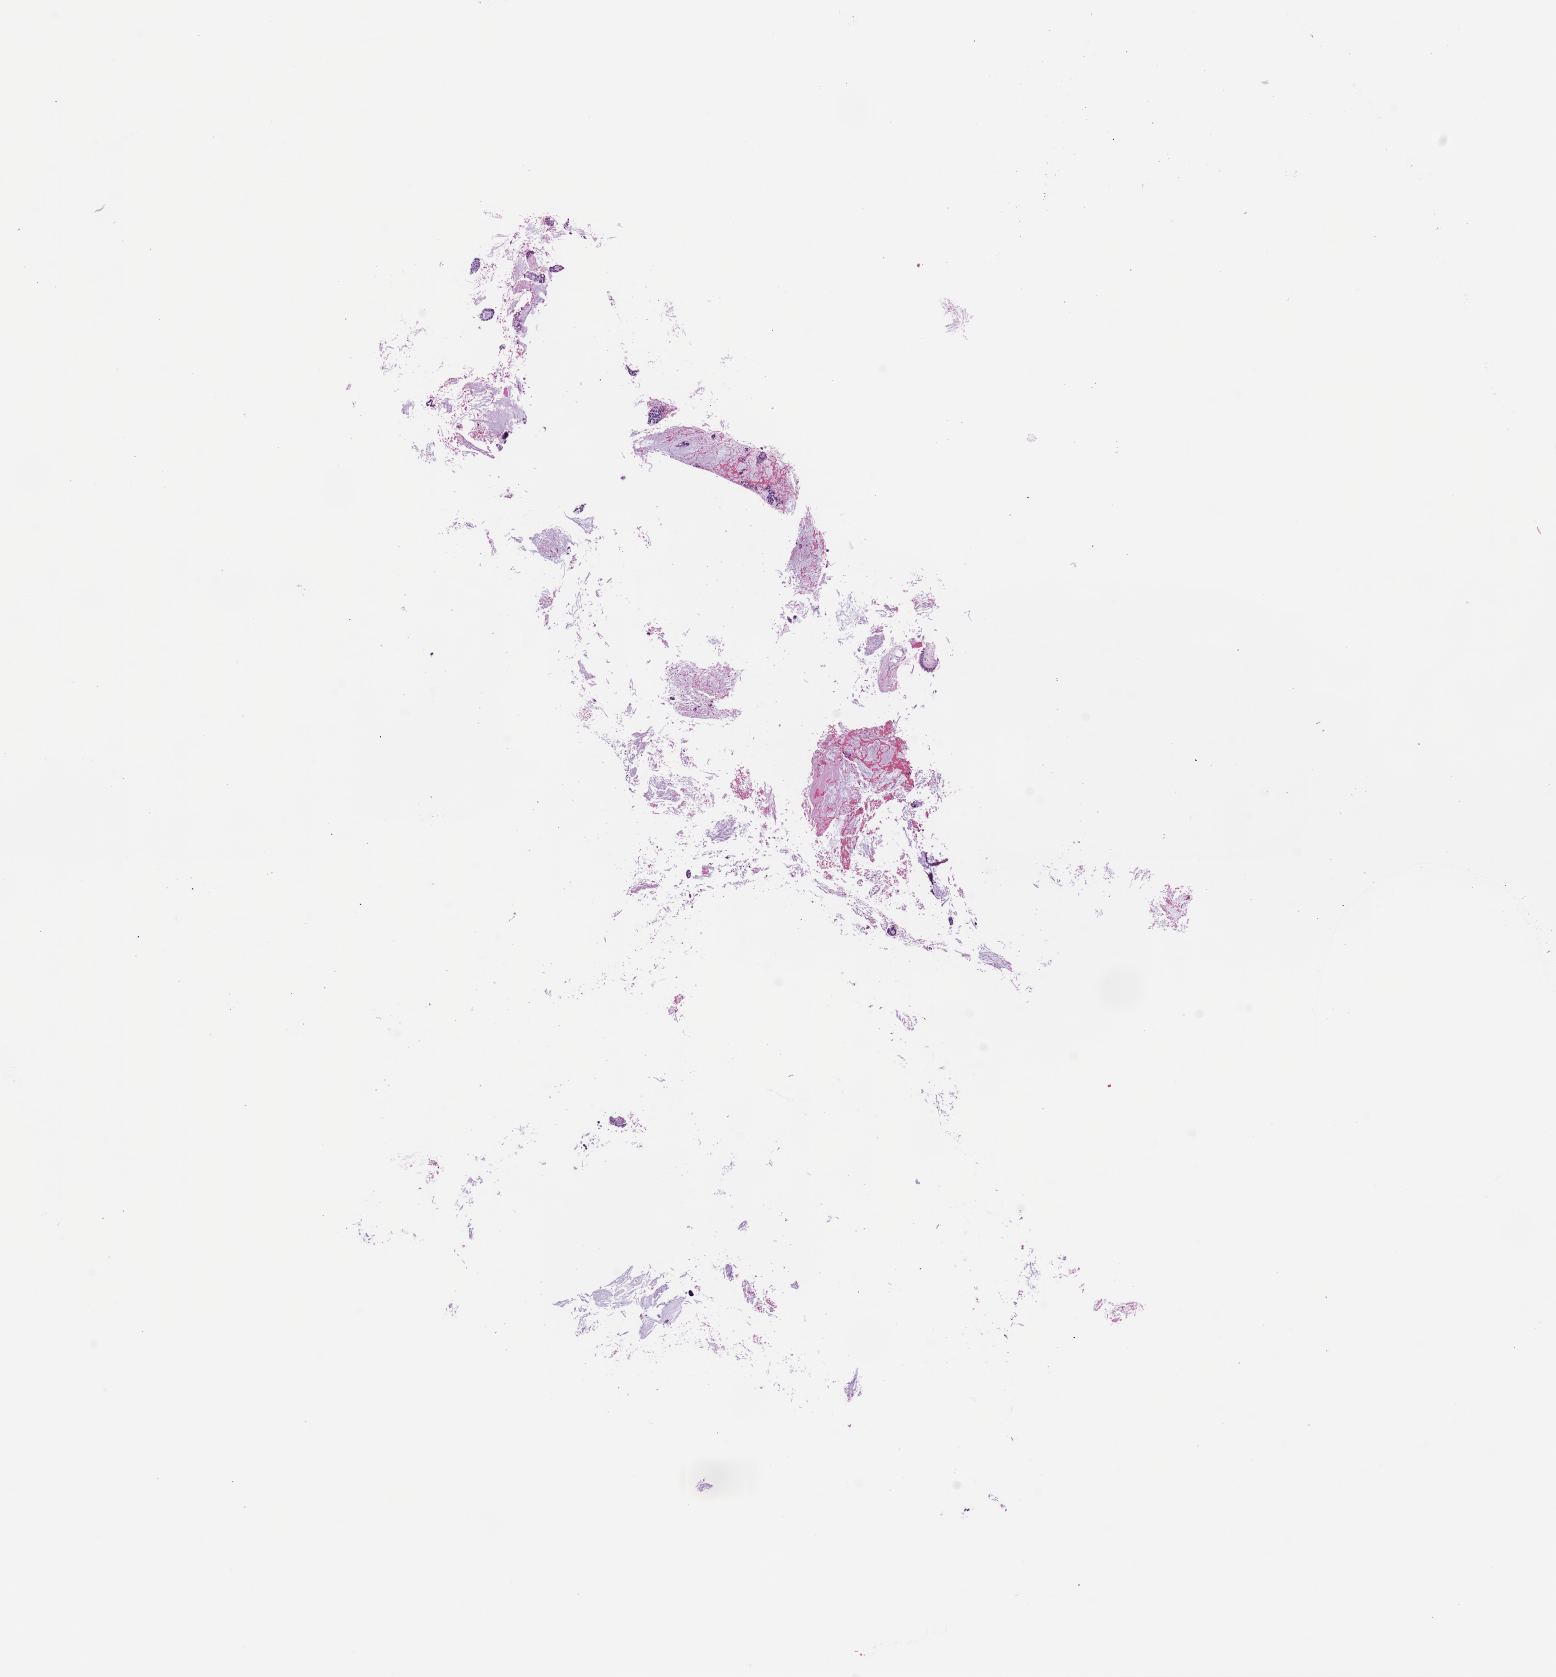
H&E whole-slide image, a low-resolution overview of the entire scanned area, about 12.6 x 13.5 mm; FFPE section; specimen time point: archival tissue. Patient sex: female.
This section: metastatic tumor tissue. Primary diagnosis of the patient: Non-Small Cell Lung Carcinoma.